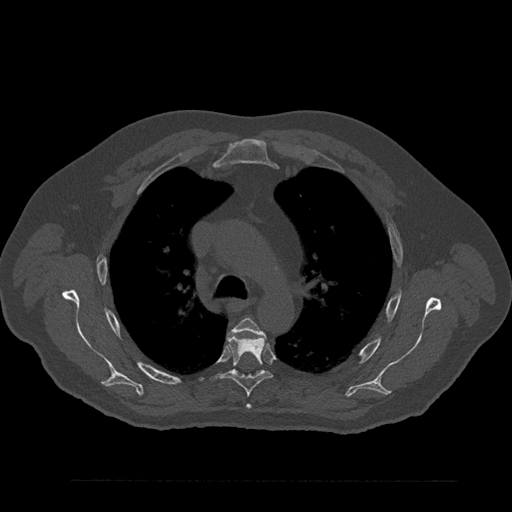
CT including the spine, one axial slice. Position 607 of 797 along the scan axis. 120 kVp. Bone window (W 1800 / L 400 HU). 0.5 mm slice thickness. 512 × 512 image matrix. Male patient, age 61 years. Case-level facts recorded for this patient, not image findings: primary cancer: prostate.
Annotated regions visible in this slice (semi-automatic segmentation, software-assisted and operator-edited):
- T4 vertebra: bounding box [x1, y1, x2, y2] px = [234, 318, 265, 410]
- T5 vertebra: [211, 335, 272, 397]
- T6 vertebra: [259, 373, 262, 376]